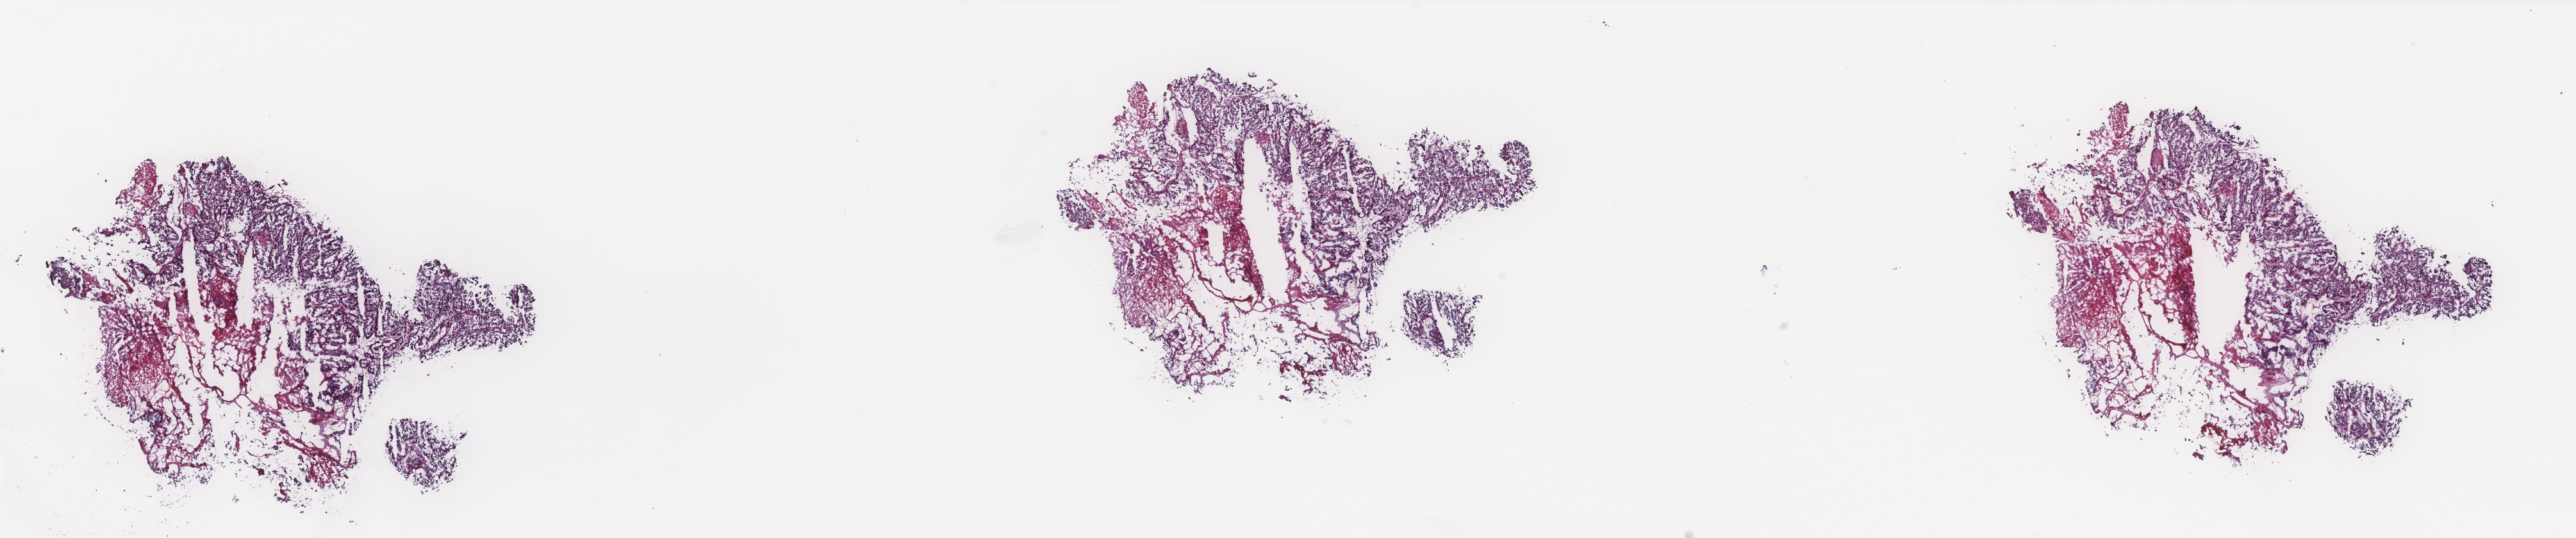
Hematoxylin and eosin (H&E) stained whole-slide image — whole scanned area (about 32.2 x 6.7 mm) shown as a low-resolution overview. Frozen section from the top of the tissue portion. Uterus, primary tumour sample. Patient: female, age at initial diagnosis 76 years. Histologic grade: G3 (poorly differentiated). Slide review estimates, as recorded: tumour cells 80%, tumour nuclei 80%, normal cells 0%, stromal cells 0%, necrosis 20%. Inflammatory infiltration, as recorded: lymphocyte infiltration 0%, monocyte infiltration 0%, neutrophil infiltration 0%.
Lymph nodes positive (case pathology): 0 of 5 examined. FIGO stage: IA. Diagnosis: Serous cystadenocarcinoma, NOS (endometrium).